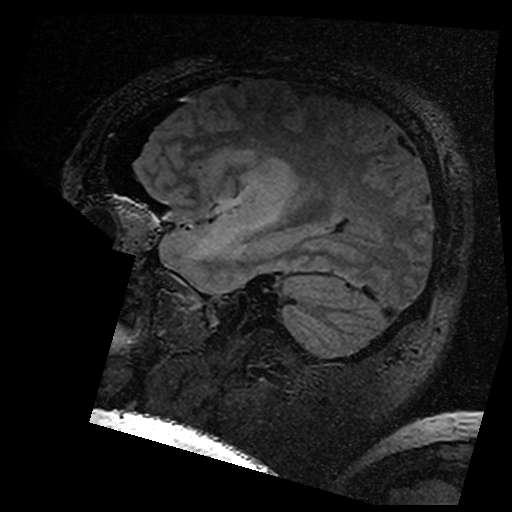
Brain MRI from a brain-tumour surgery series, one sagittal slice; position 122 of 176 along the scan axis; T2 FLAIR; 1 mm slice thickness; 512 × 512 image matrix, field of view 250 × 250 mm. From the clinical record (not read from this slice): histopathology: Astrocytoma; WHO grade: 3; IDH mutation: yes.
Annotated regions visible in this slice (manually delineated by an expert):
- residual tumour: bounding box <211,146,293,201> (left, top, right, bottom; pixels)